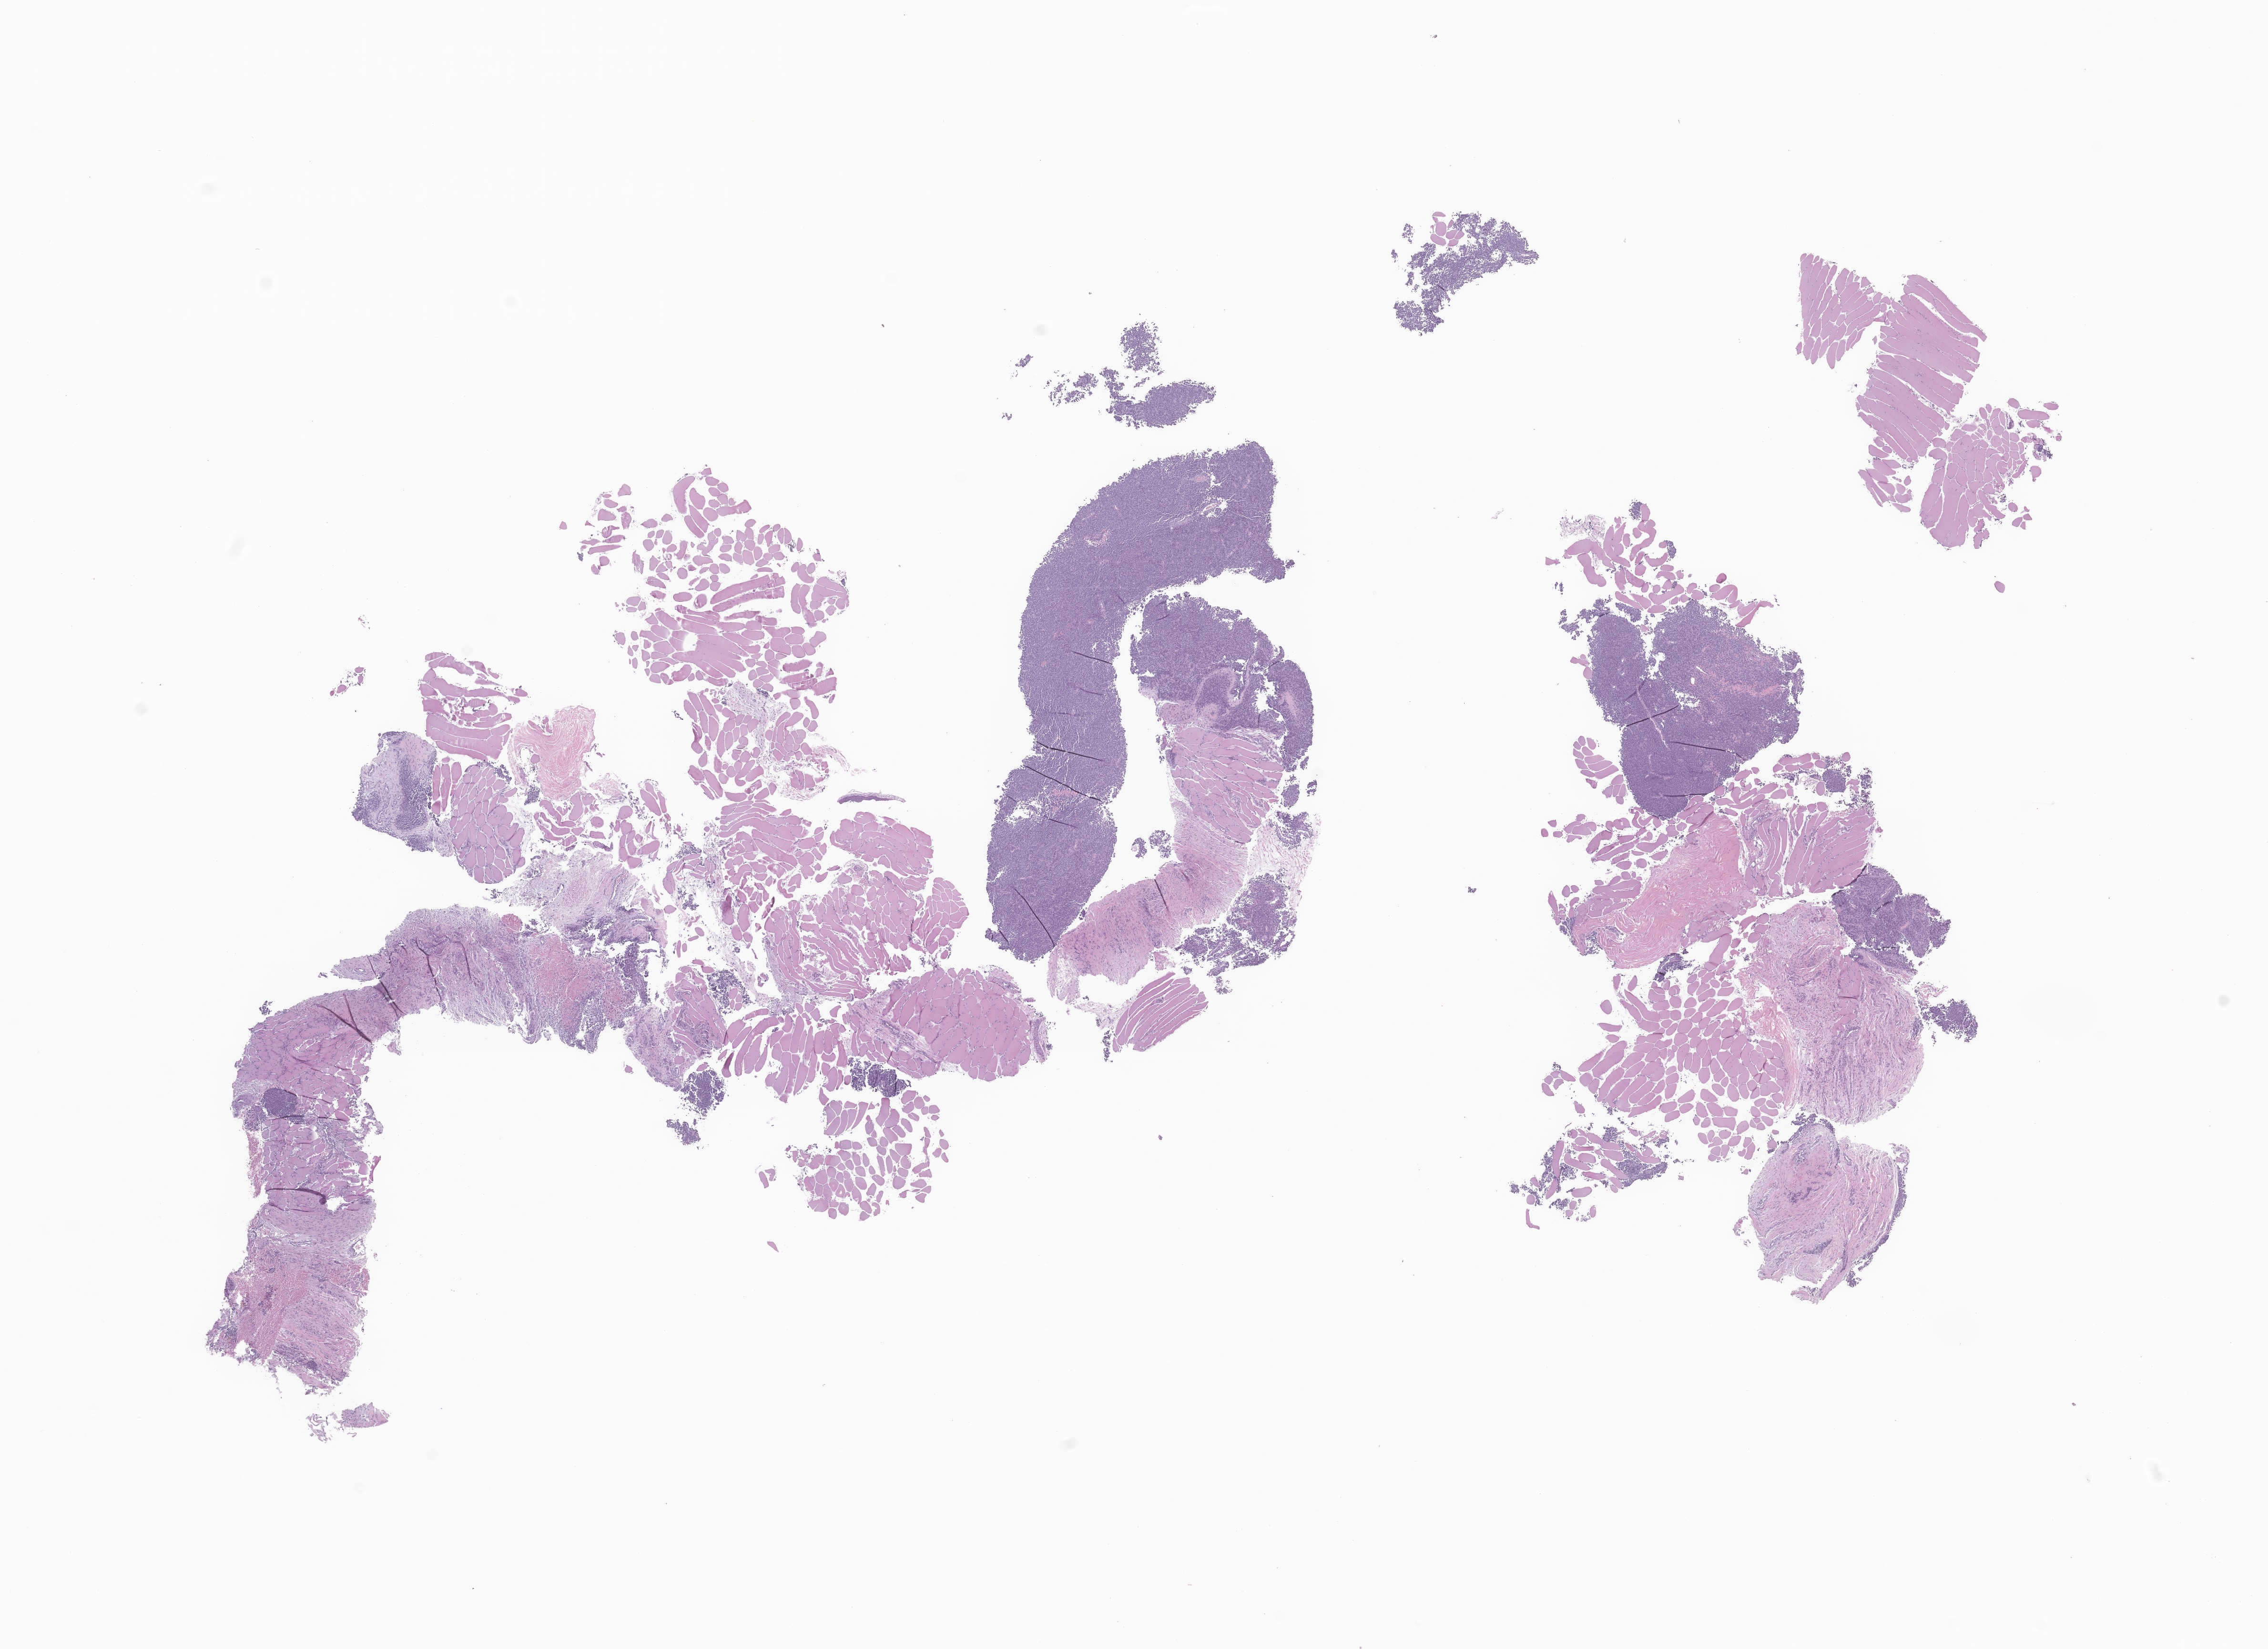
Haematoxylin and eosin whole-slide image of tumor tissue from the soft tissue of lower extremity — a low-resolution overview of the entire scanned area, about 20.1 x 14.6 mm. Patient: male, age 213 months.
Specimen: formalin-fixed, paraffin-embedded (FFPE) tissue.